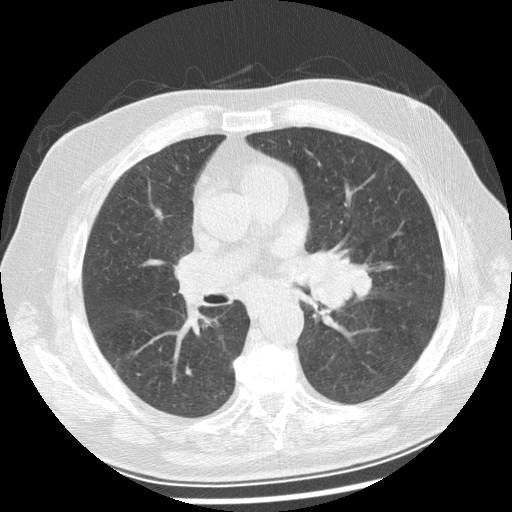
Low-dose screening chest CT, axial slice; first (baseline) screen; lung window (W 1500 / L -600 HU); 2.5 mm slice thickness; standard (soft-tissue) reconstruction kernel (STANDARD); slice 112 of 250 in the series; 512 × 512 image matrix. Male participant, aged 70 years at enrolment.
Lesion marked by an expert reader, bounding box [x1, y1, x2, y2] px = [286, 241, 369, 316]. No non-calcified nodule or mass ≥4 mm was recorded by the screening reader at this exam. Official screen result: positive, change unspecified: nodule(s) >= 4 mm or enlarging nodule(s), mass(es), or other non-specific abnormalities suspicious for lung cancer. Participant outcome: lung cancer diagnosed 29 days after this screen — squamous cell carcinoma, keratinizing, NOS, left main stem bronchus, moderately differentiated (G2), stage IIIB (AJCC 6th edition), 40 mm at pathology.